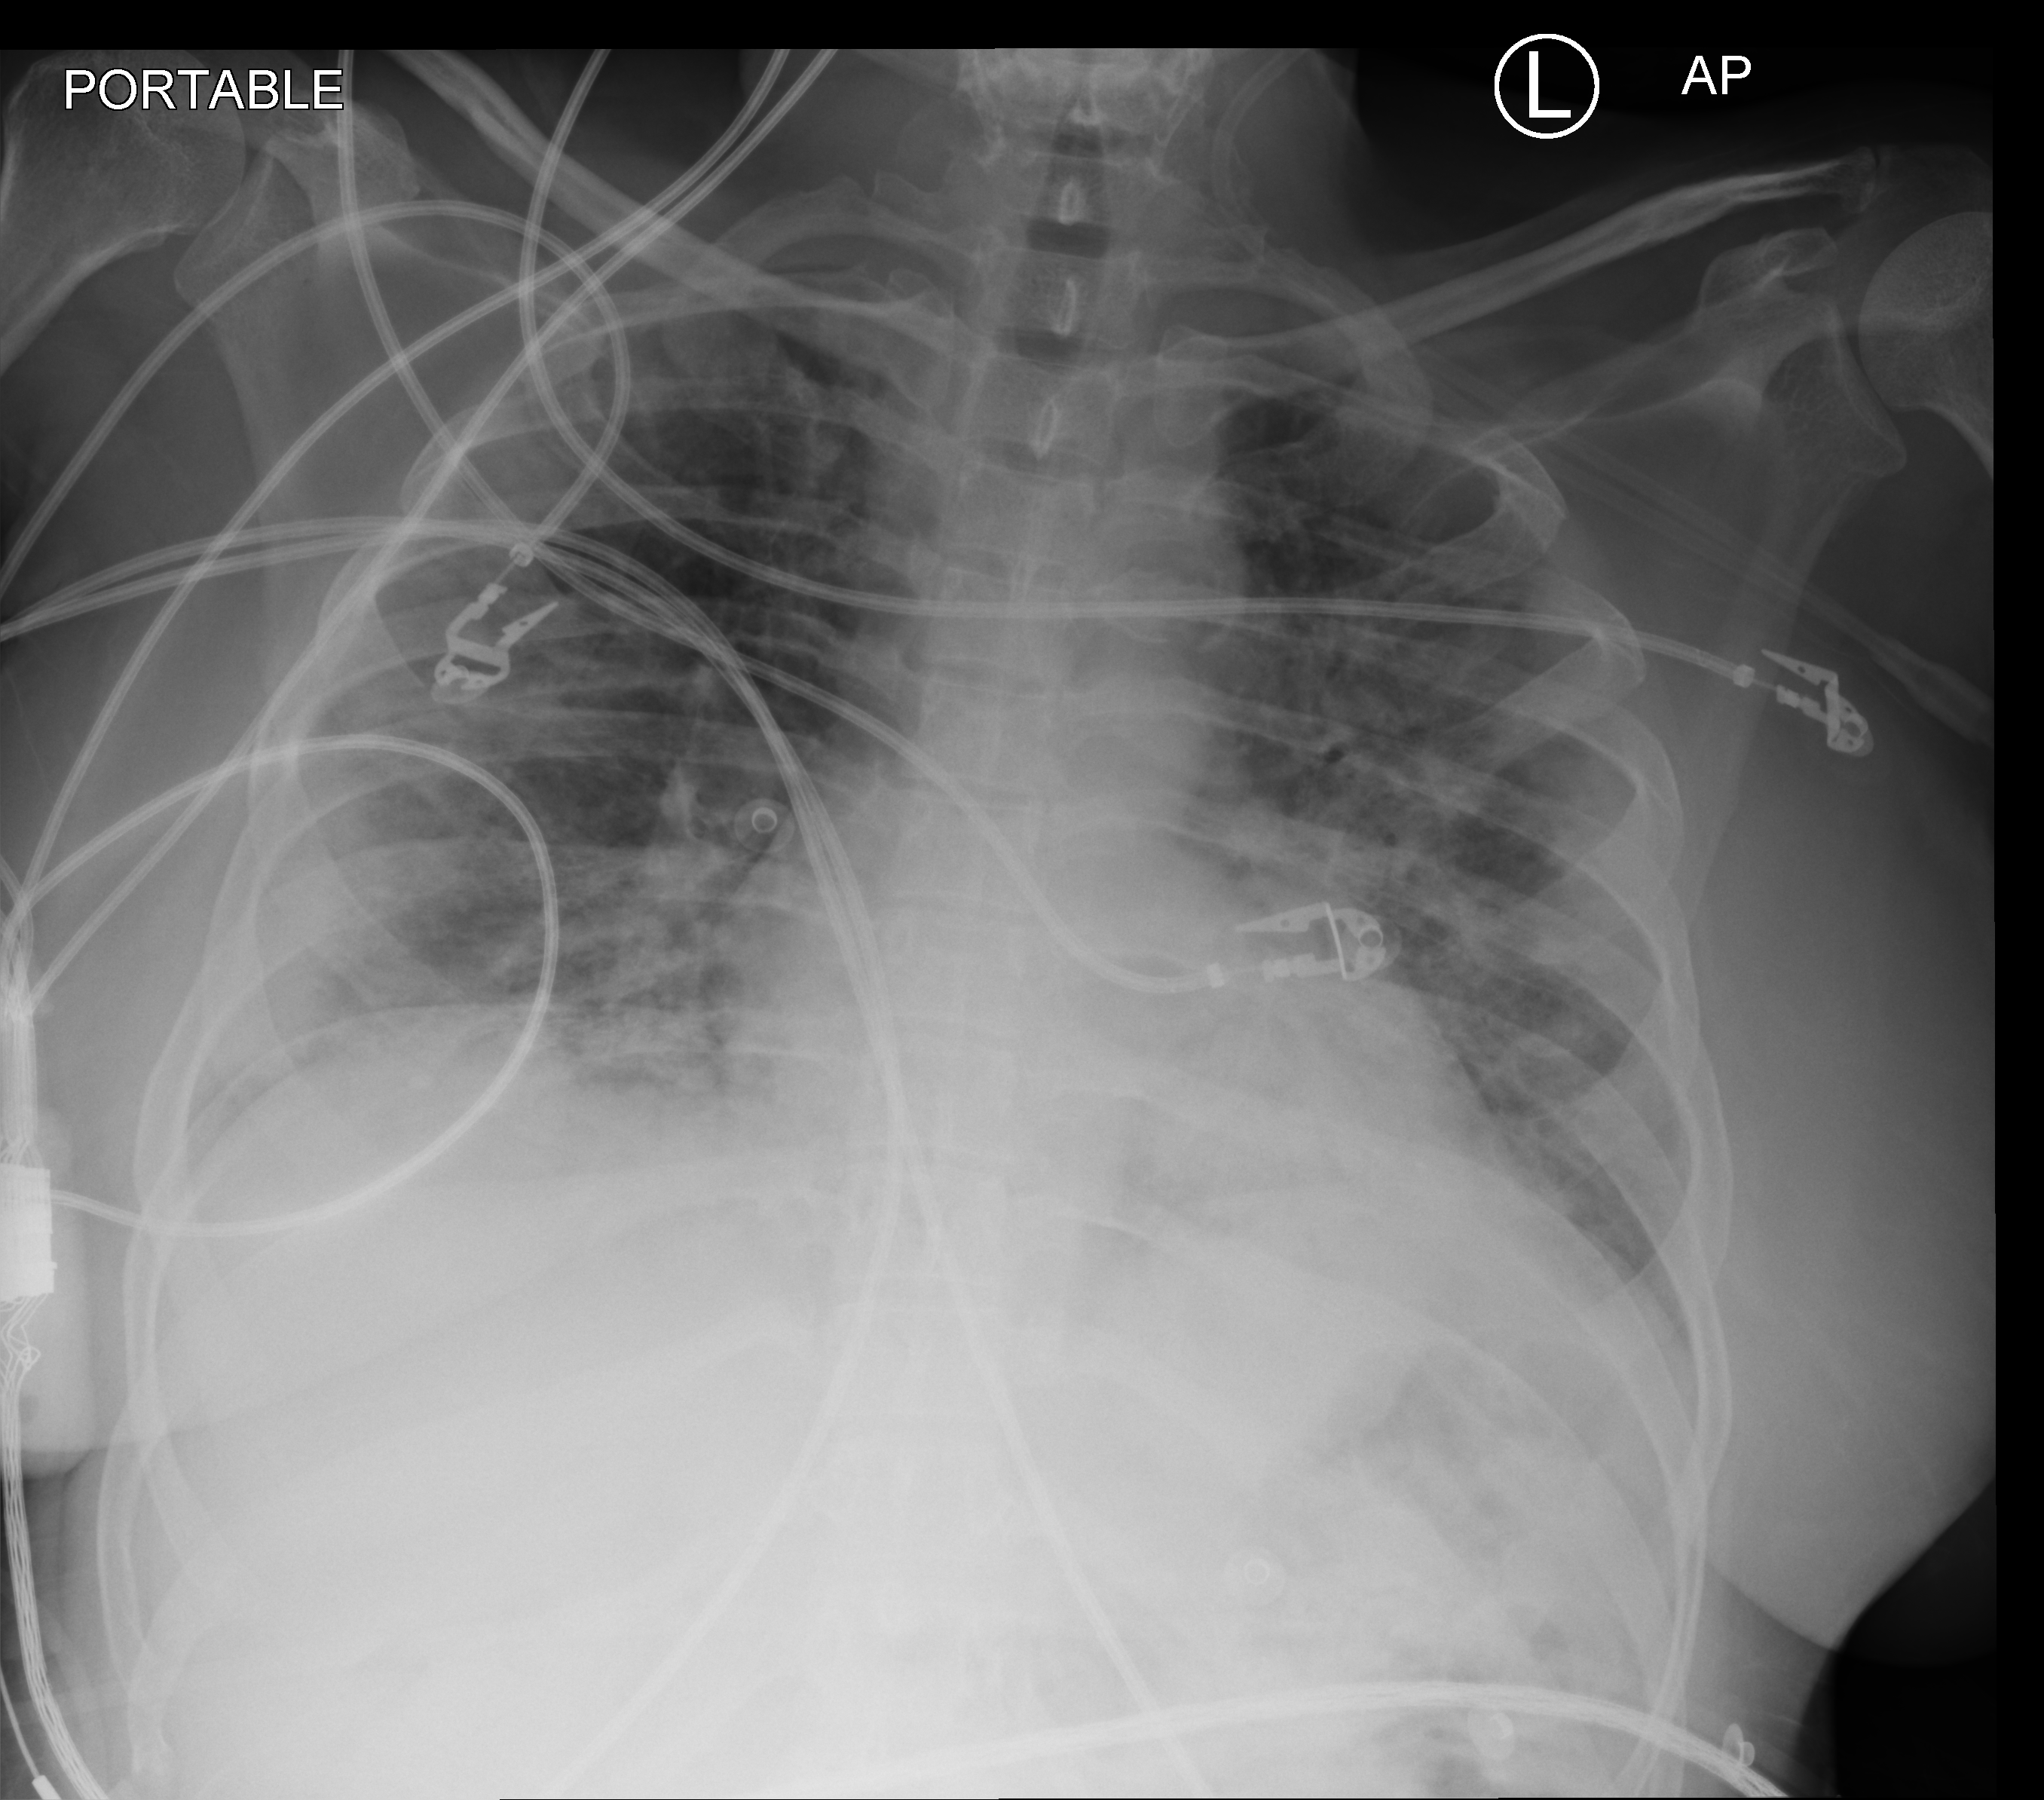
Bedside chest radiograph (computed radiography); anteroposterior (AP) projection. Patient hospitalised with COVID-19, aged 18–59 years.
Admission-level facts for this patient (not findings on this image; timing relative to this image not recorded): mechanically ventilated during this hospital stay: yes; chronic kidney disease (admission record): no.